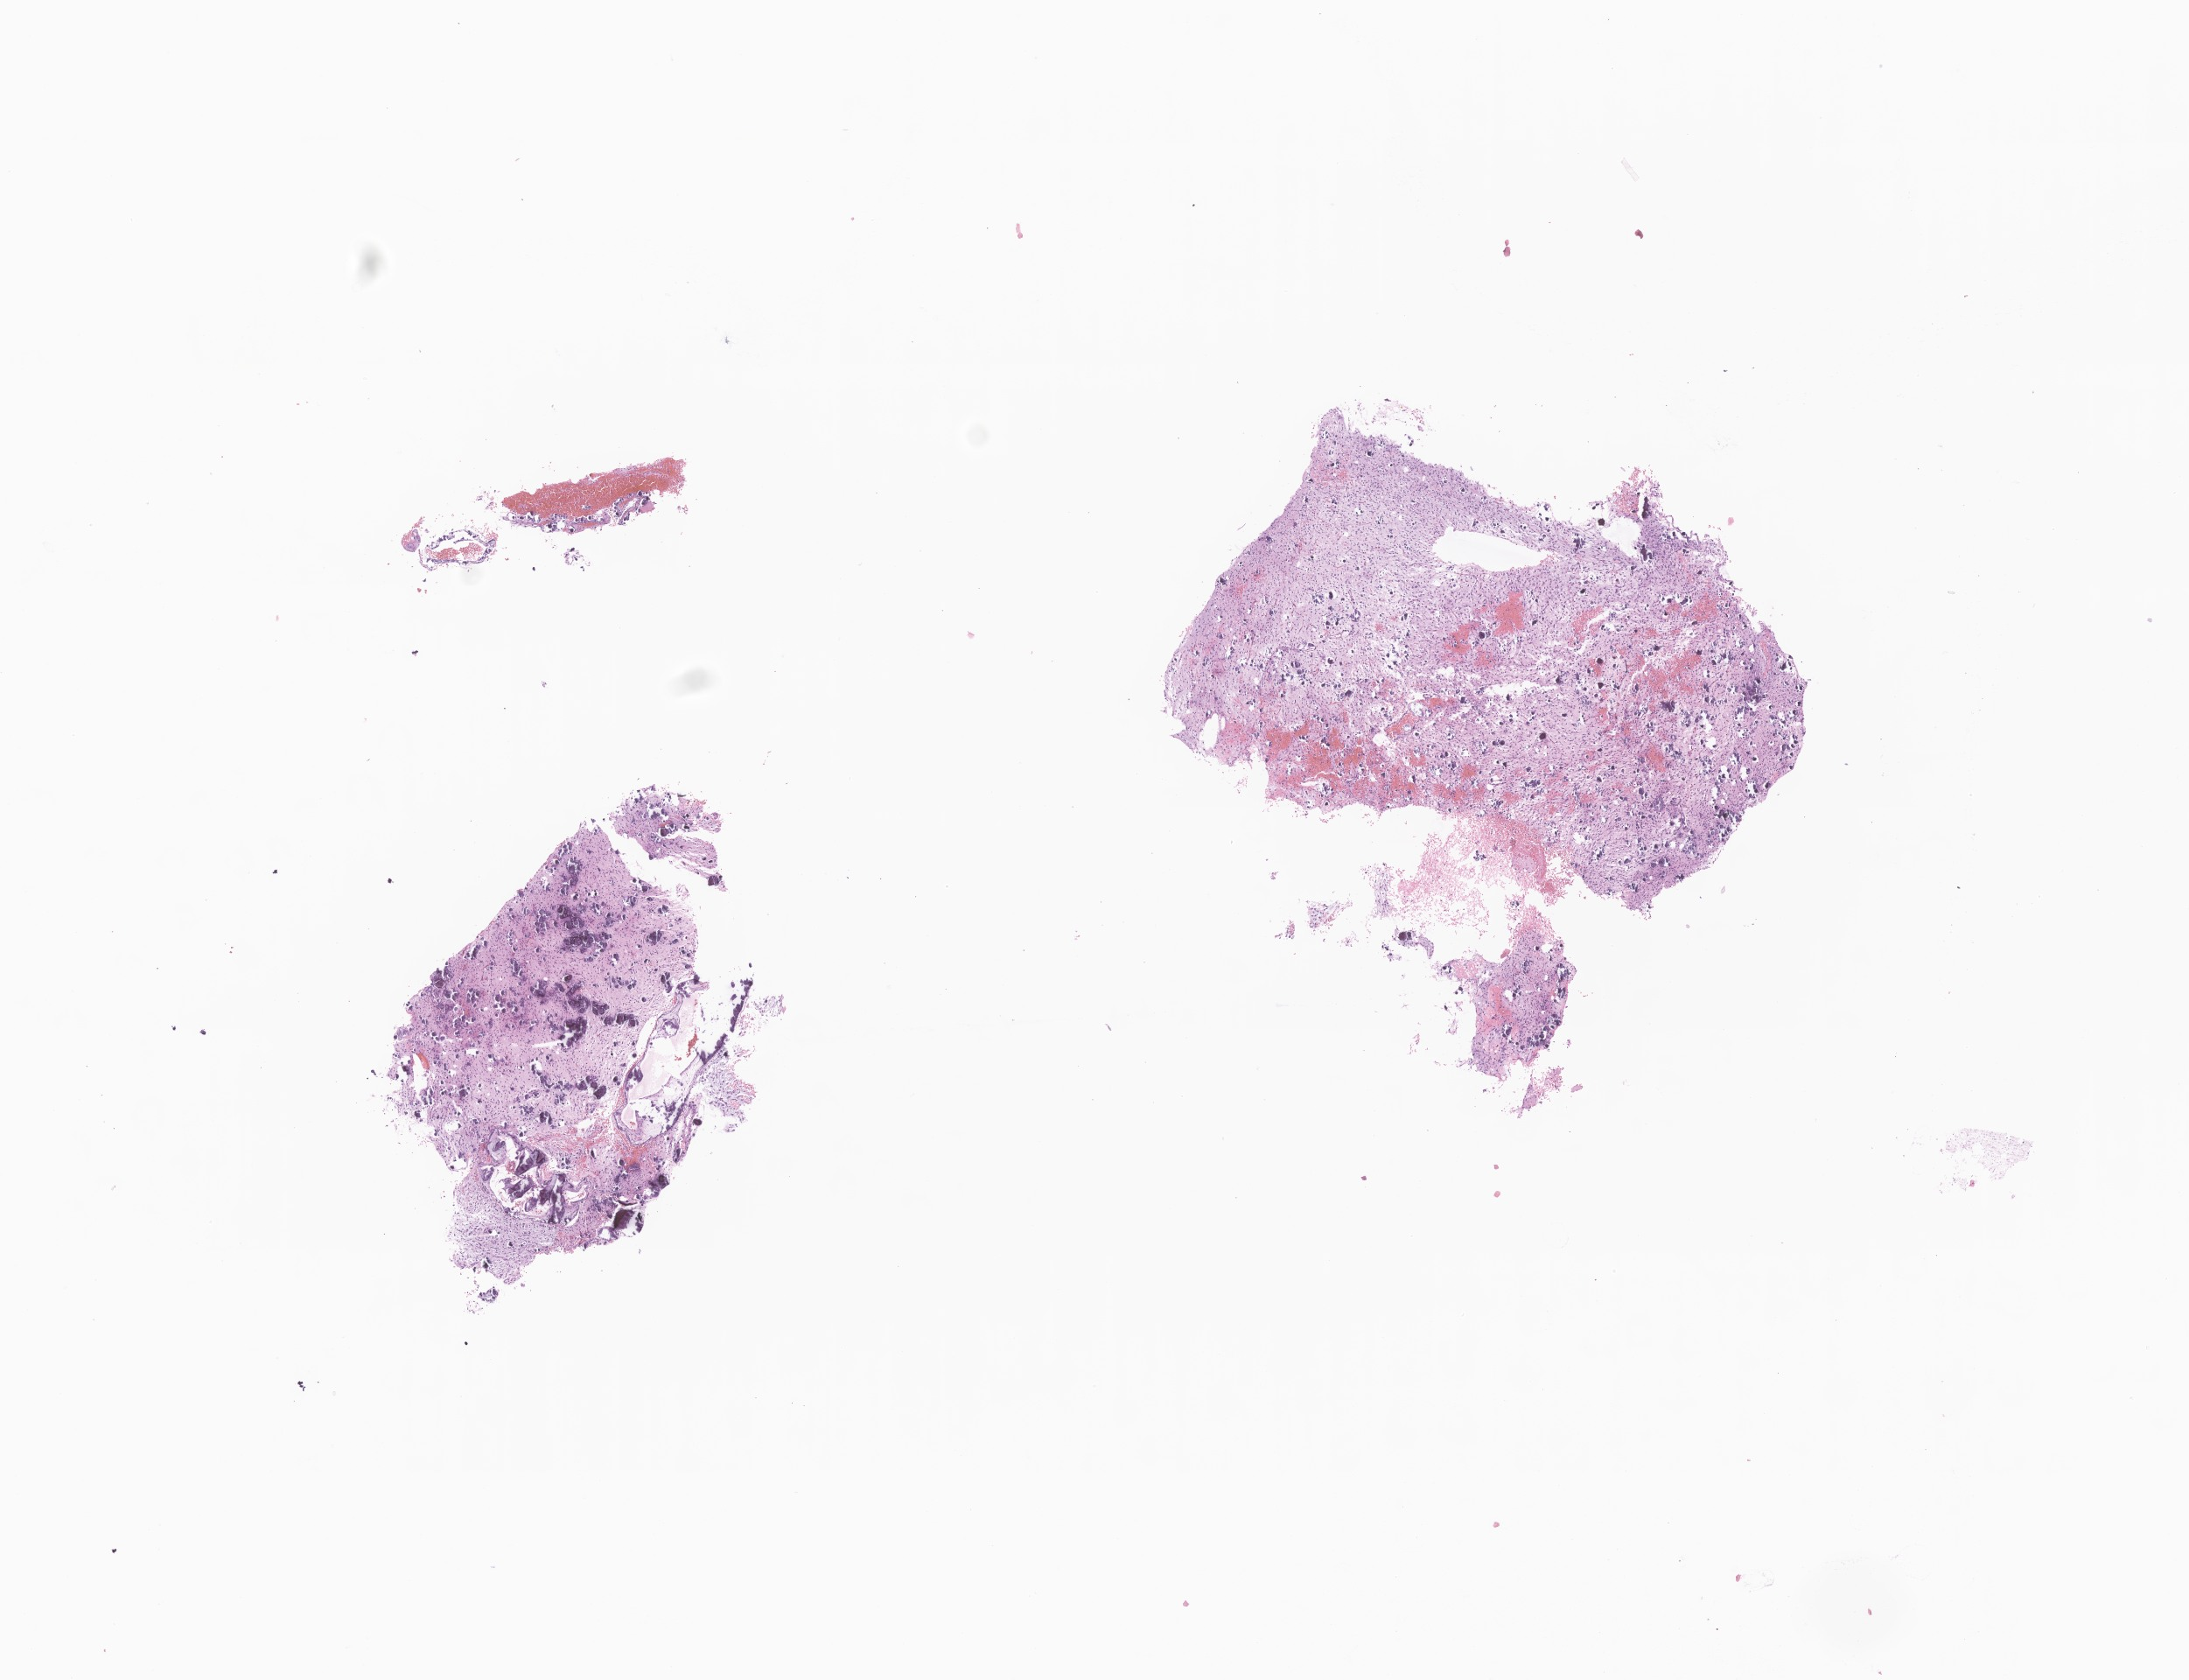
Whole-slide image, hematoxylin and eosin (H&E) stain of tumor tissue from the brain — whole scanned area (about 10.5 x 8.1 mm) shown as a low-resolution overview, formalin-fixed, paraffin-embedded (FFPE) tissue. Patient: female, age 198 months (16 years 6 months).
* diagnosis (ICD-O-3 morphology term): Glioma, malignant